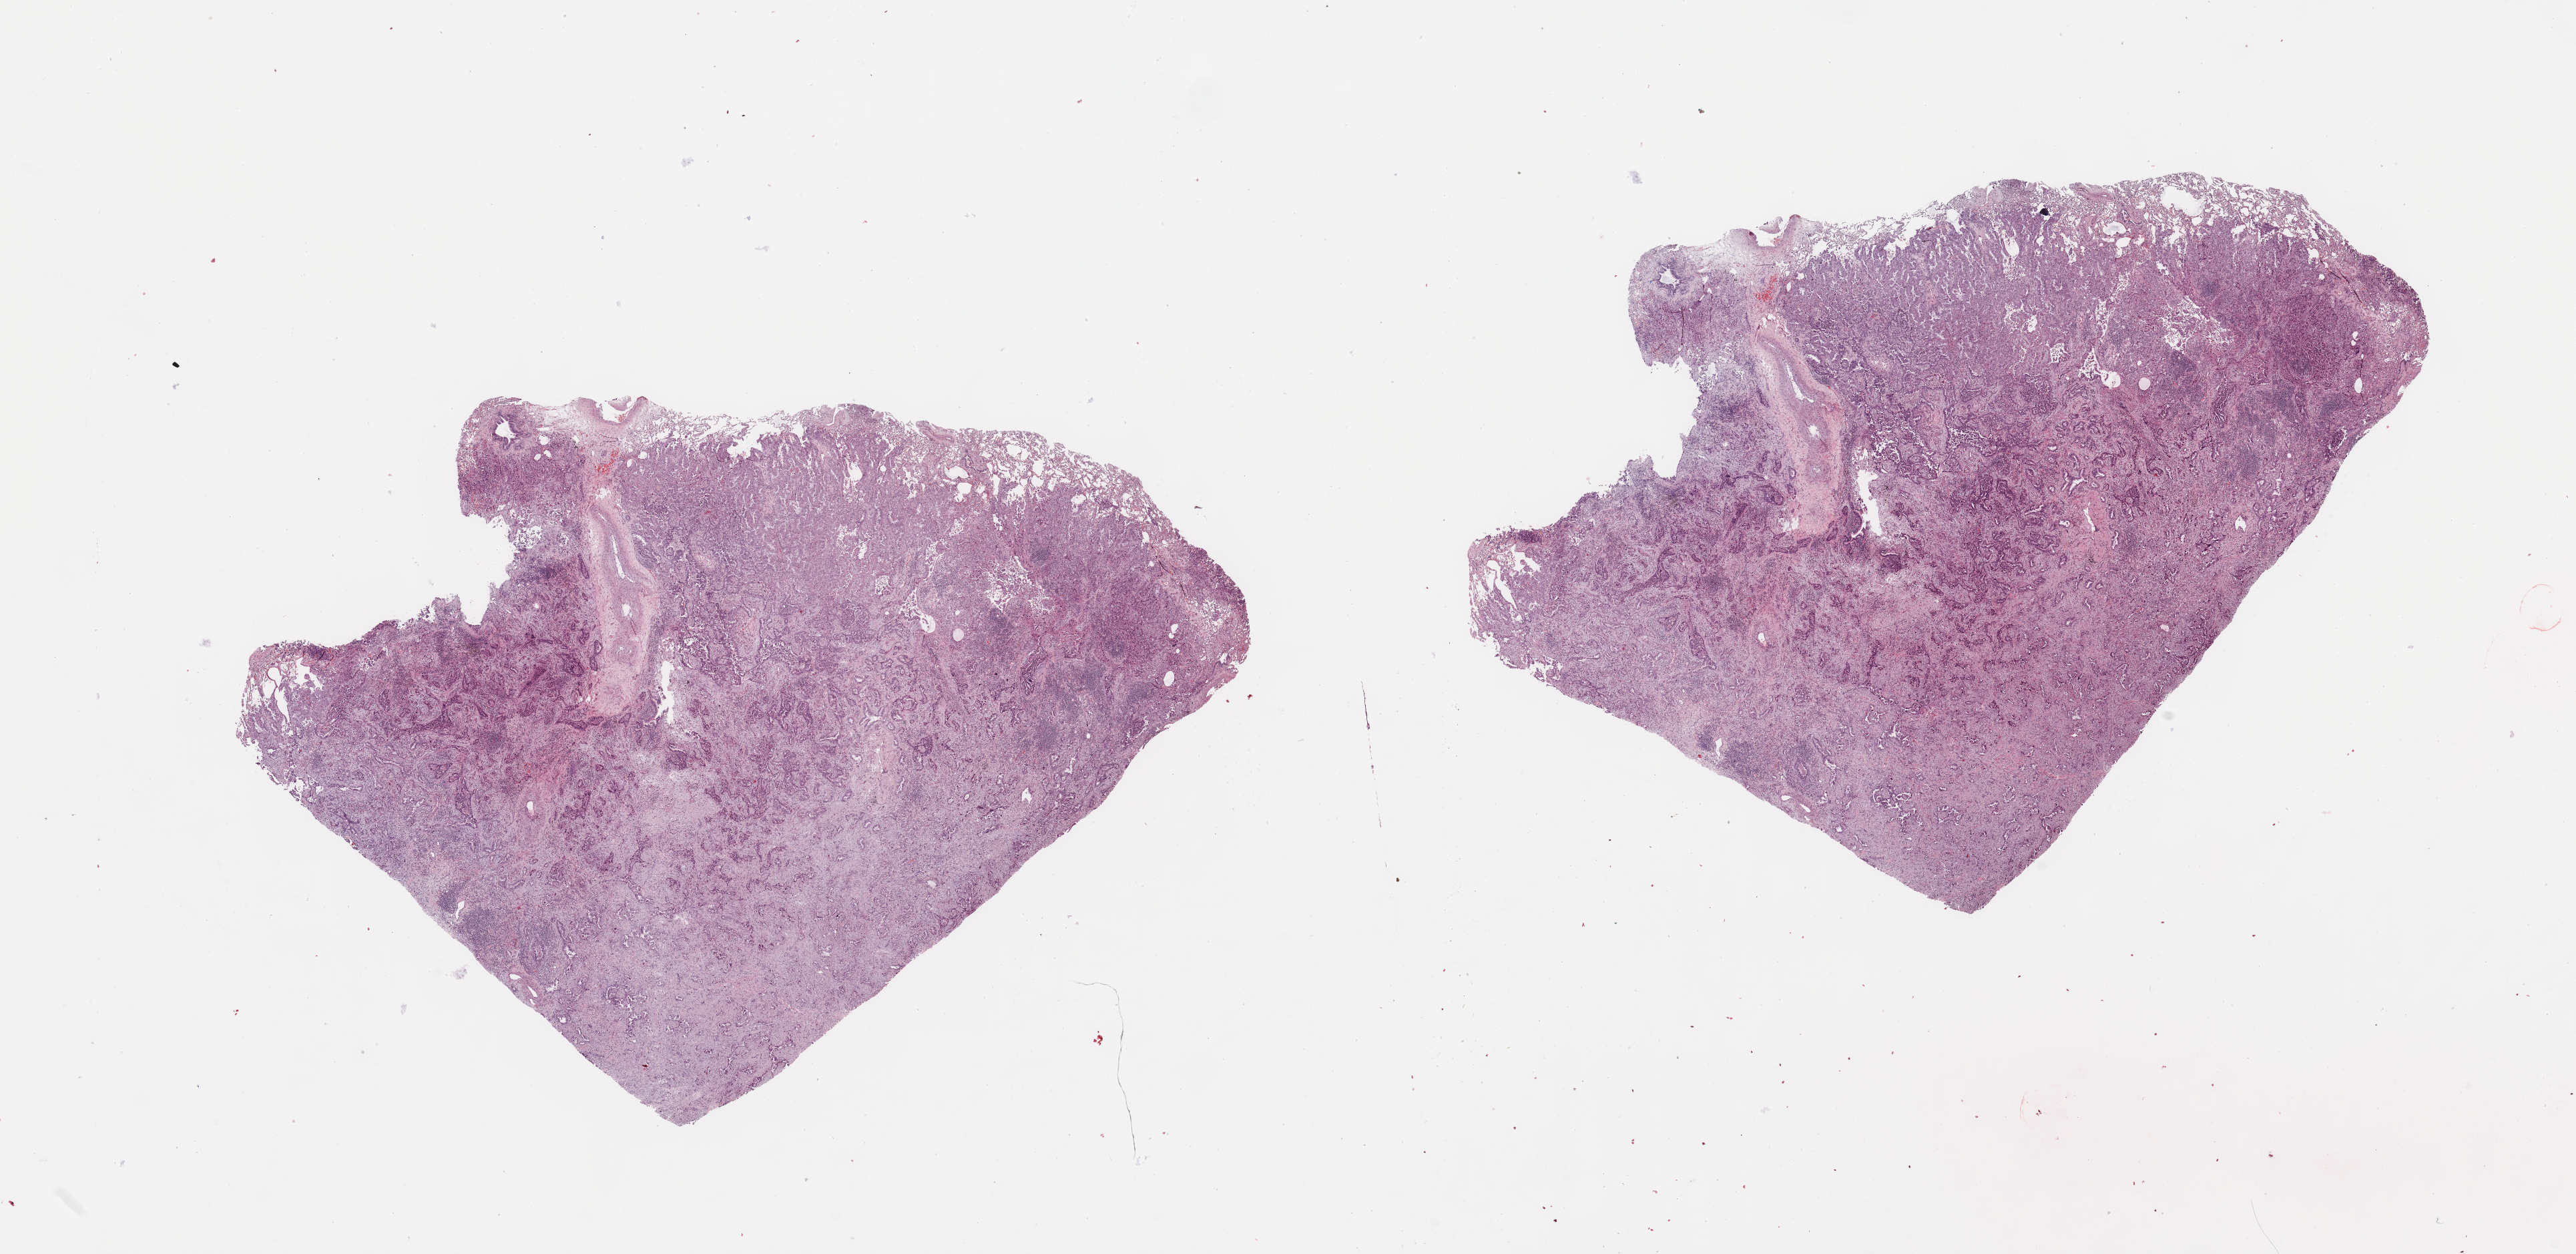
Whole-slide histology image, Hematoxylin and eosin (H&E) stained — low-resolution overview of the scanned area, about 30.5 x 14.9 mm (acquisition: 20x scan); tumour tissue sample, lung. Patient: female, age 67 years. Histologic grade: G2 (moderately differentiated).
- AJCC pathologic stage: II
- diagnosis: Adenocarcinoma, NOS